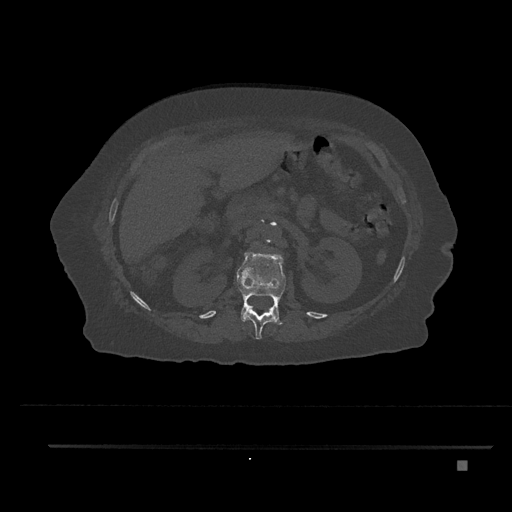
CT including the spine, one axial slice. Slice 237 of 797 in the series (ordered by position). Reconstruction kernel Br40s/3. Bone window (W 1800 / L 400 HU). 512 × 512 image matrix, field of view 437 × 437 mm. Female patient, age 76 years. From the clinical record (not read from this slice): primary cancer: lung.
Outlined on this slice (semi-automatic segmentation, software-assisted and operator-edited):
- L1 vertebra: box from (x=237, y=250) to (x=286, y=325) px
- T12 vertebra: (x=245, y=306)–(x=275, y=340)